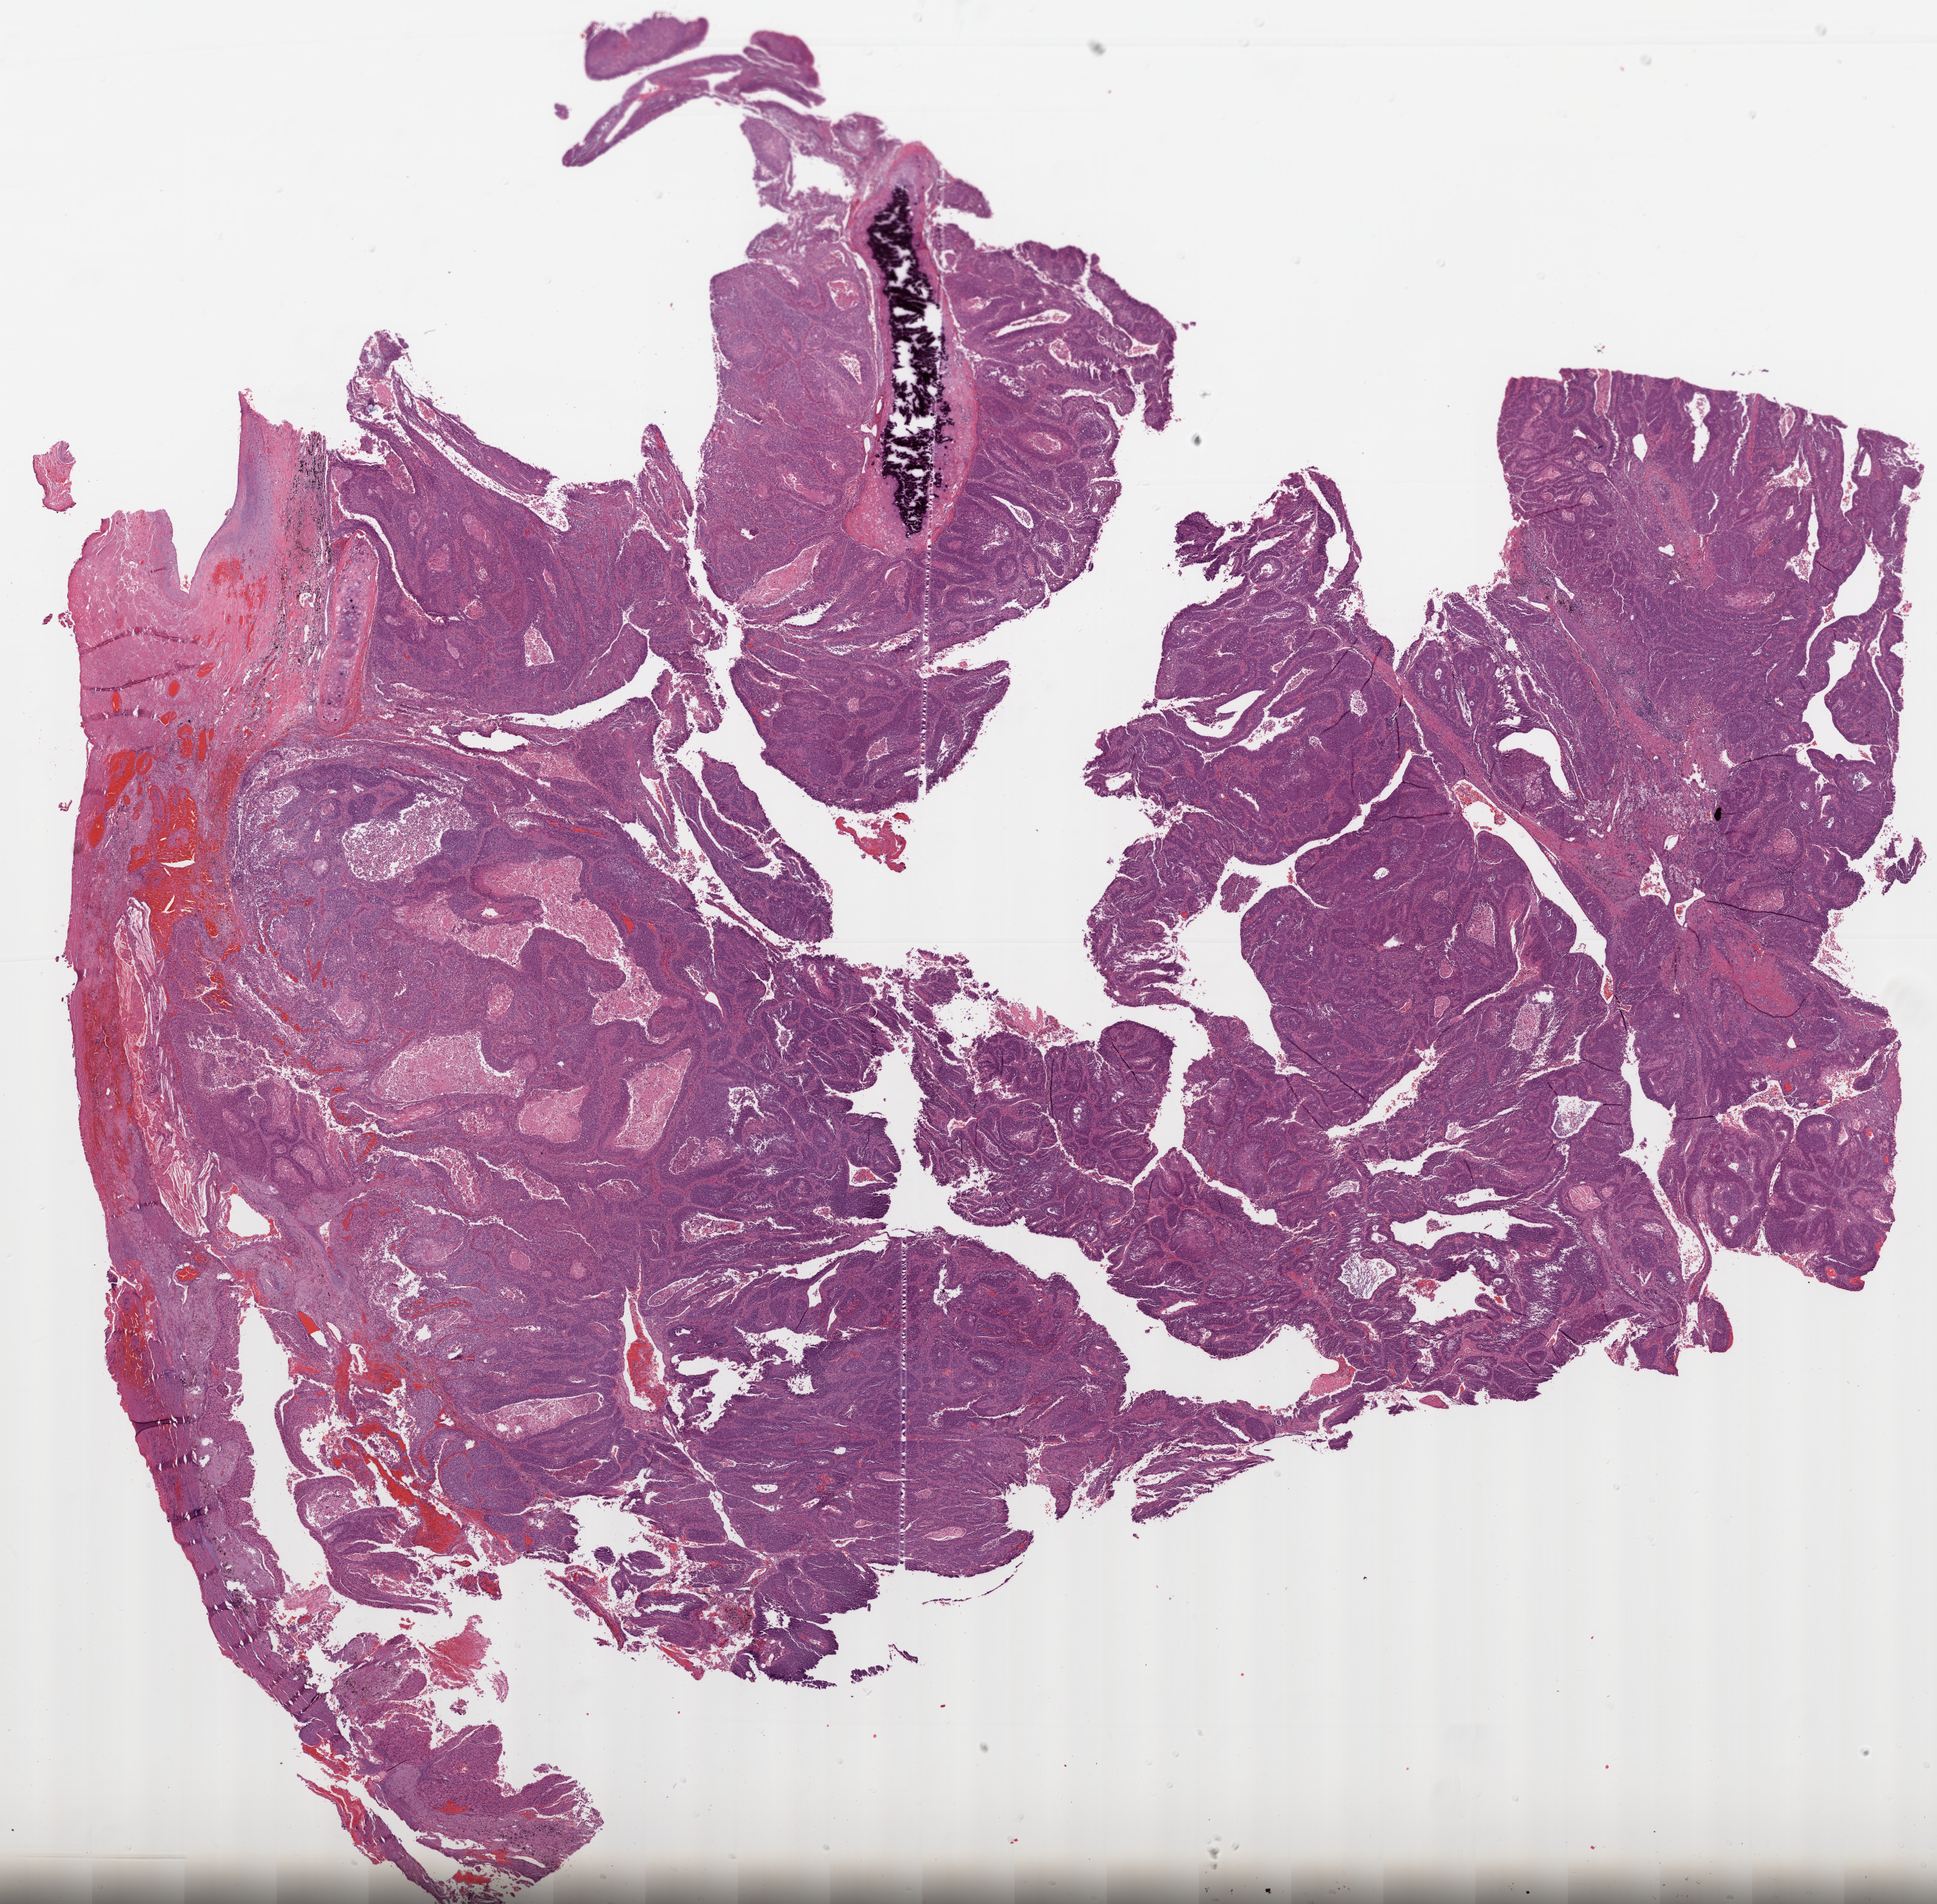
Digitized H&E-stained tissue section (whole slide) — low-resolution overview of the scanned area, about 21.1 x 20.7 mm (slide scanned at 20x). Formalin-fixed paraffin-embedded (FFPE) diagnostic section. Lung, primary tumour sample. Female, age 76 years at initial diagnosis.
AJCC pathologic stage: IIA. TNM: T2 N0 M0. Diagnosis: Squamous cell carcinoma, NOS (upper lobe, lung).